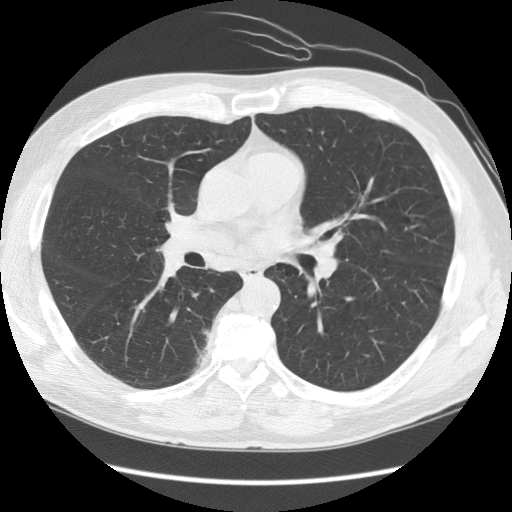
Axial slice from a low-dose chest CT screening exam. First (baseline) screen. Lung window (W 1500 / L -600 HU). Standard (soft-tissue) reconstruction kernel (STANDARD). Slice 61 of 141 in the series. Male, age 69 years at enrolment. Former smoker at enrolment.
Lesion marked by an expert reader, bounding box <164,316,226,375> (left, top, right, bottom; pixels). No non-calcified nodule or mass ≥4 mm was recorded by the screening reader at this exam. Later outcome: lung cancer diagnosed 497 days after this screen (after the second annual screen) — bronchiolo-alveolar adenocarcinoma, NOS, right lower lobe, well differentiated (G1), stage IB (AJCC 6th edition), 23 mm at pathology.